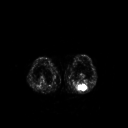
FDG PET of an extremity soft-tissue mass (from a PET/CT study), one axial slice. Slice 176 of 267 in the series (ordered by position). 128 × 128 image matrix, field of view 500 × 500 mm. Patient: male, 54 years. From the clinical record (not read from this slice): histological type: synovial sarcoma; site of the primary tumour: left poplietal fossa.
Structures marked on this image (expert contour drawn on MRI and transferred to this co-registered scan by the dataset authors):
- gross tumour volume (mass): bounding box [x1, y1, x2, y2] px = [78, 84, 88, 91]